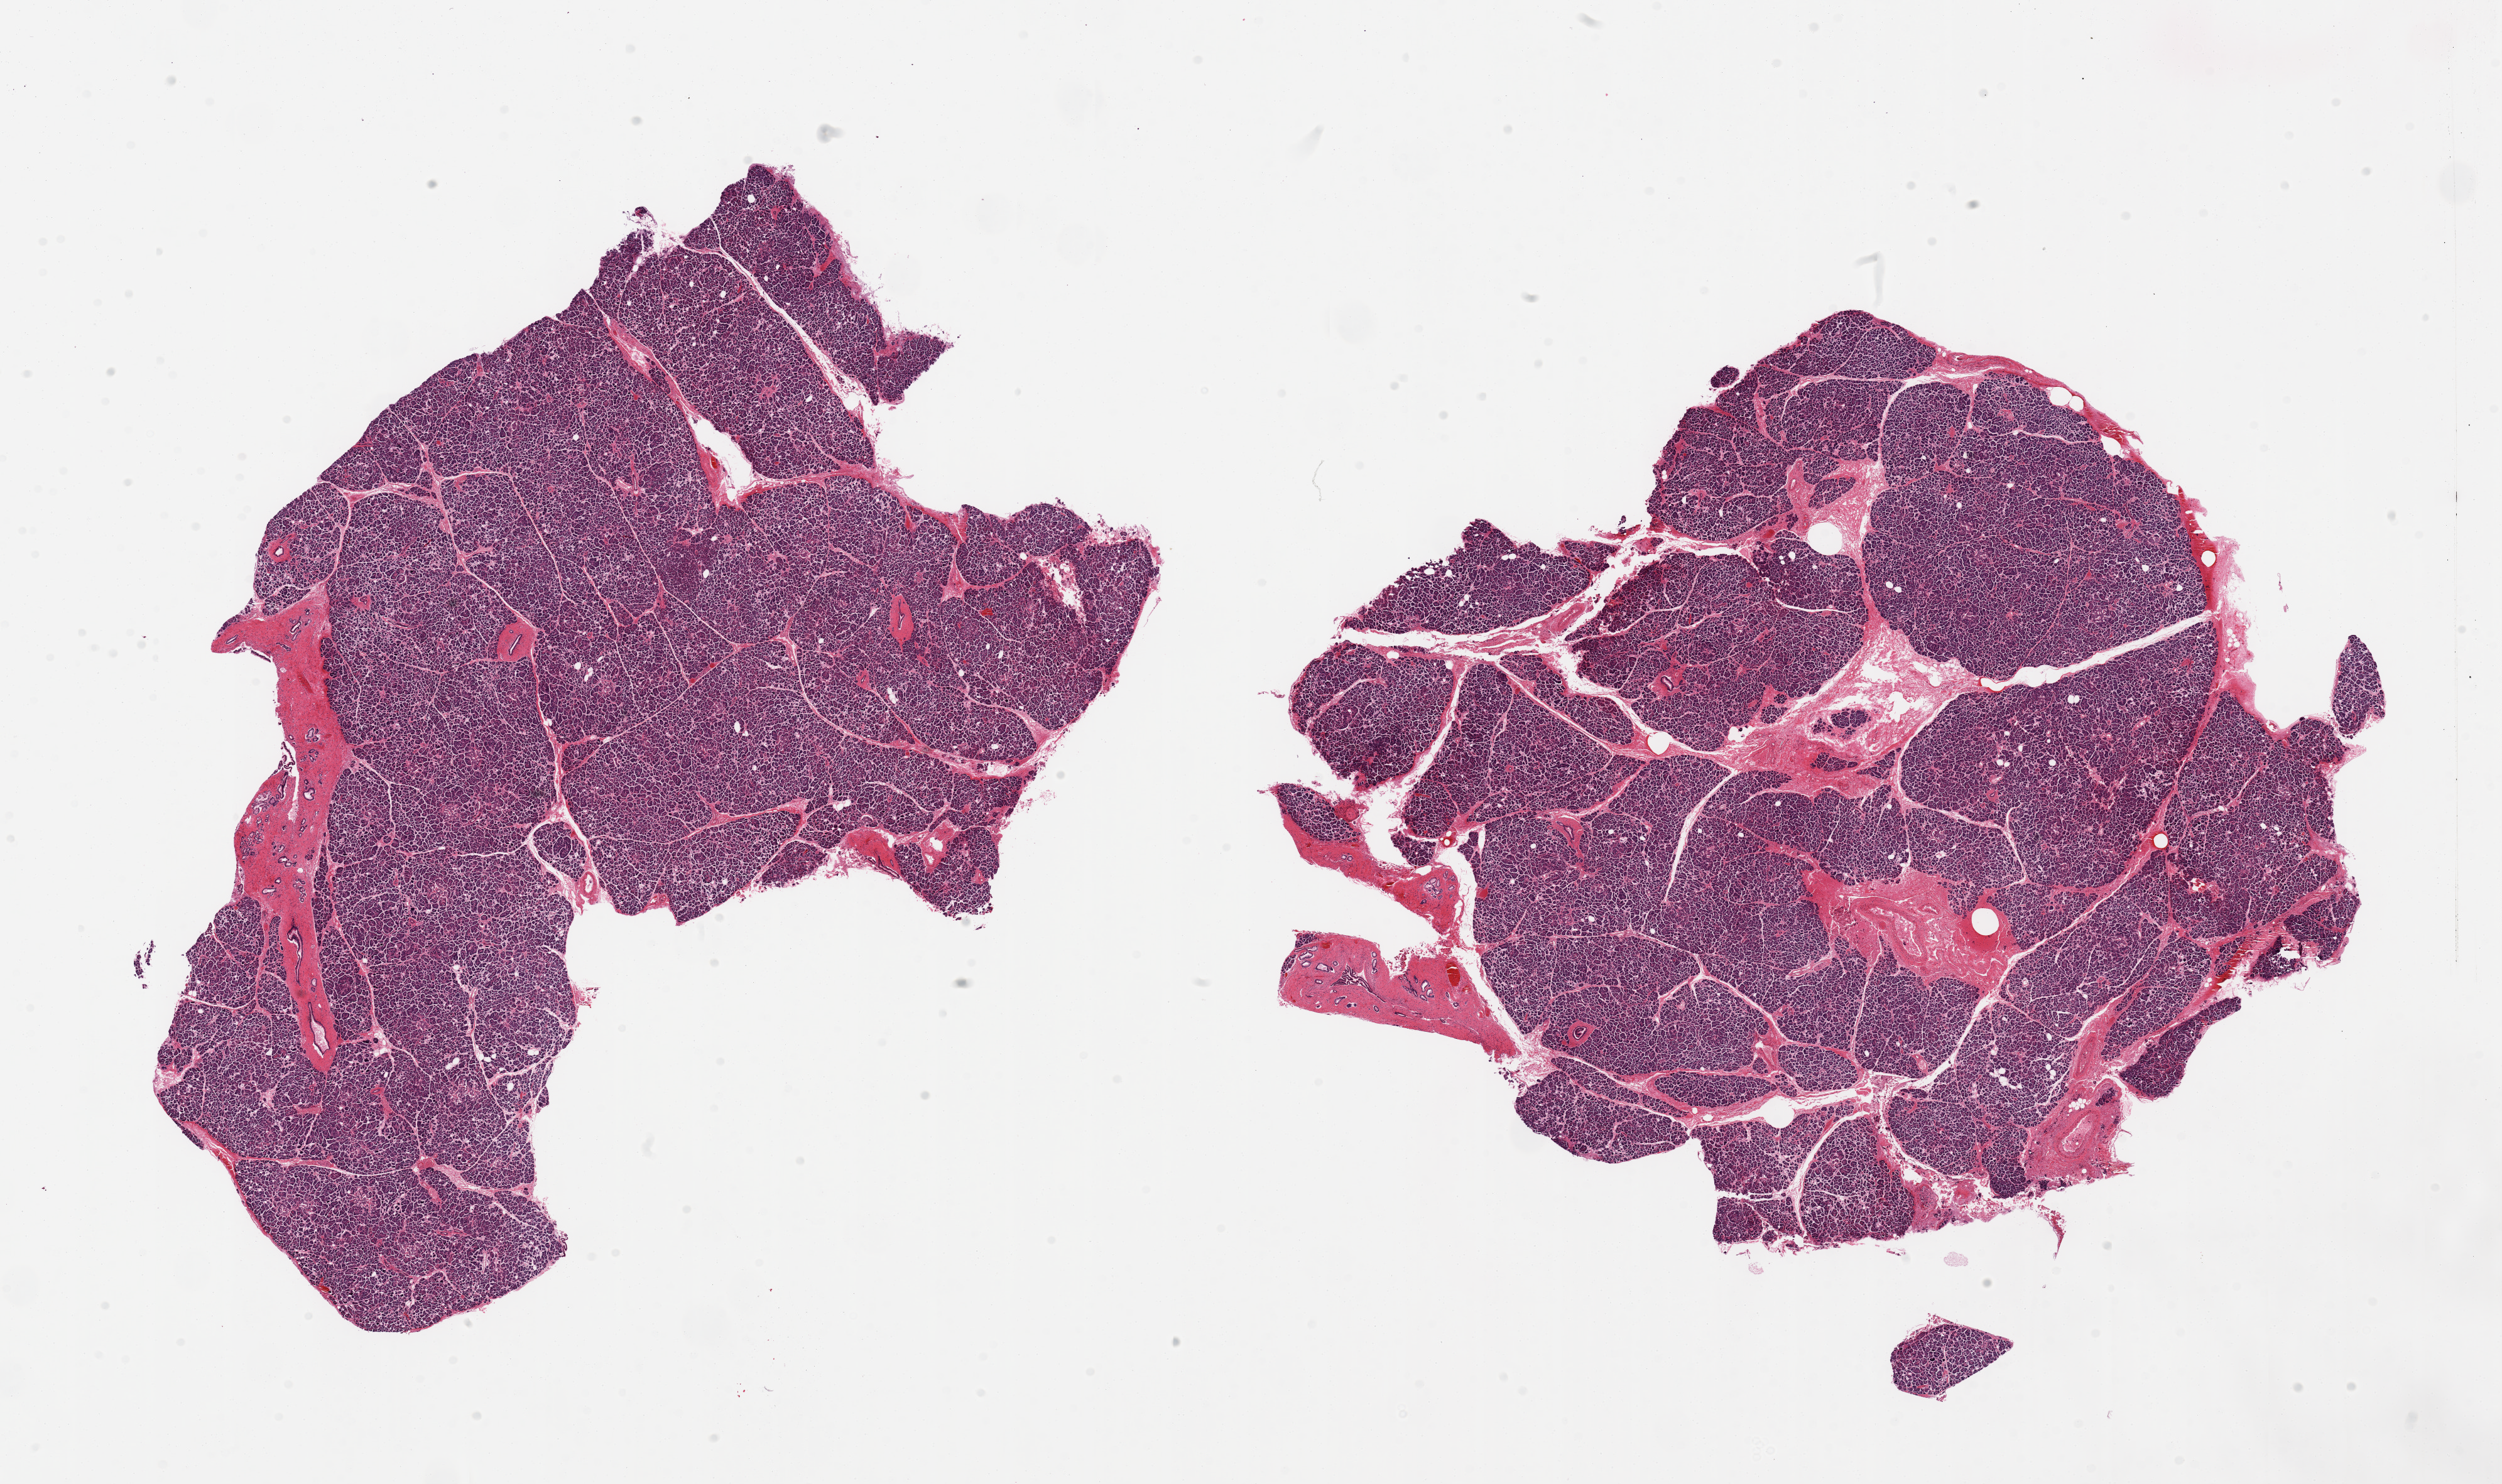
Digitized hematoxylin and eosin (H&E)-stained section — a low-resolution overview of the entire scanned area, about 31.5 x 18.7 mm (acquisition: 20x scan). PAXgene-fixed paraffin-embedded (PFPE) section. Section of pancreas (target tissue). Tissue donor sample. Donor: female.
Pathologist's review note for this sample: 2 pieces.